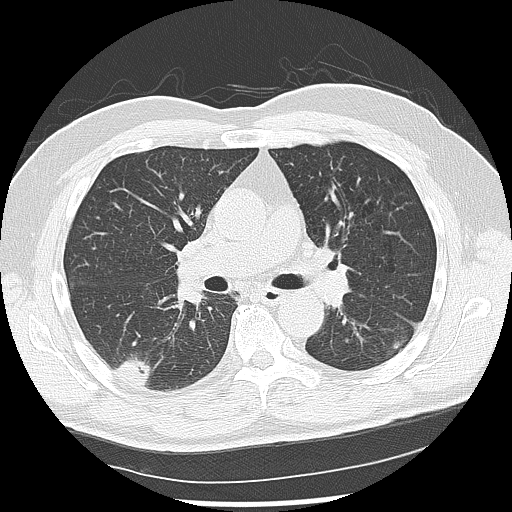
Low-dose screening chest CT, one axial slice; position 77 of 142 along the scan axis; reconstruction kernel LUNG; 120 kVp; lung window (W 1500 / L -600 HU); 2.5 mm slice thickness; 512 × 512 image matrix.
Annotated regions visible in this slice (expert manual segmentation):
- lesion 1 (nodule, lower lobe of left lung): bounding box [x1, y1, x2, y2] px = [394, 341, 404, 351]
- lesion 2 (nodule, lower lobe of right lung): [115, 358, 151, 385]